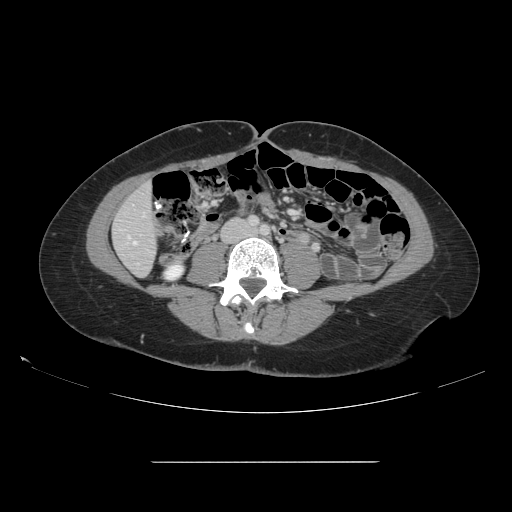
Contrast-enhanced abdominal CT, one axial slice. Slice 27 of 151 in the series (ordered by position). 120 kVp. Intravenous contrast given. Soft-tissue window (W 400 / L 40 HU). 2.5 mm slice thickness. 512 × 512 image matrix, field of view 421 × 421 mm. Female patient, age 46 years. From the clinical record (not read from this slice): diagnosis: colorectal cancer liver metastases, imaged before liver resection; multiple liver metastases: yes; largest metastasis: 3 cm.
Annotated regions visible in this slice (manually delineated by an expert):
- liver: box from (x=114, y=186) to (x=156, y=276) px
- planned liver remnant (the part of the liver to remain after resection): (x=114, y=186)–(x=156, y=276)